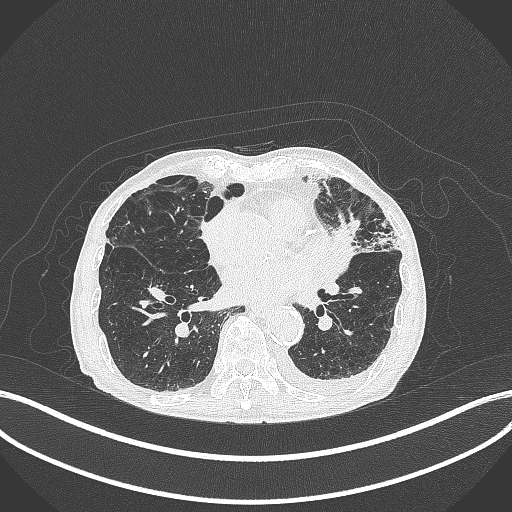
Chest CT, one axial slice; position 157 of 385 along the scan axis; 120 kVp; lung window (W 1500 / L -600 HU); 1 mm slice thickness; 512 × 512 image matrix, field of view 400 × 400 mm. Male patient, age 90 years or older. Case-level facts recorded for this patient, not image findings: clinical TNM (as recorded): T2b N1 M0.
Annotated regions visible in this slice (rectangle marked by the reading radiologist):
- lung tumour (recorded histology: squamous cell carcinoma): bounding box [x1, y1, x2, y2] px = [331, 215, 365, 266]